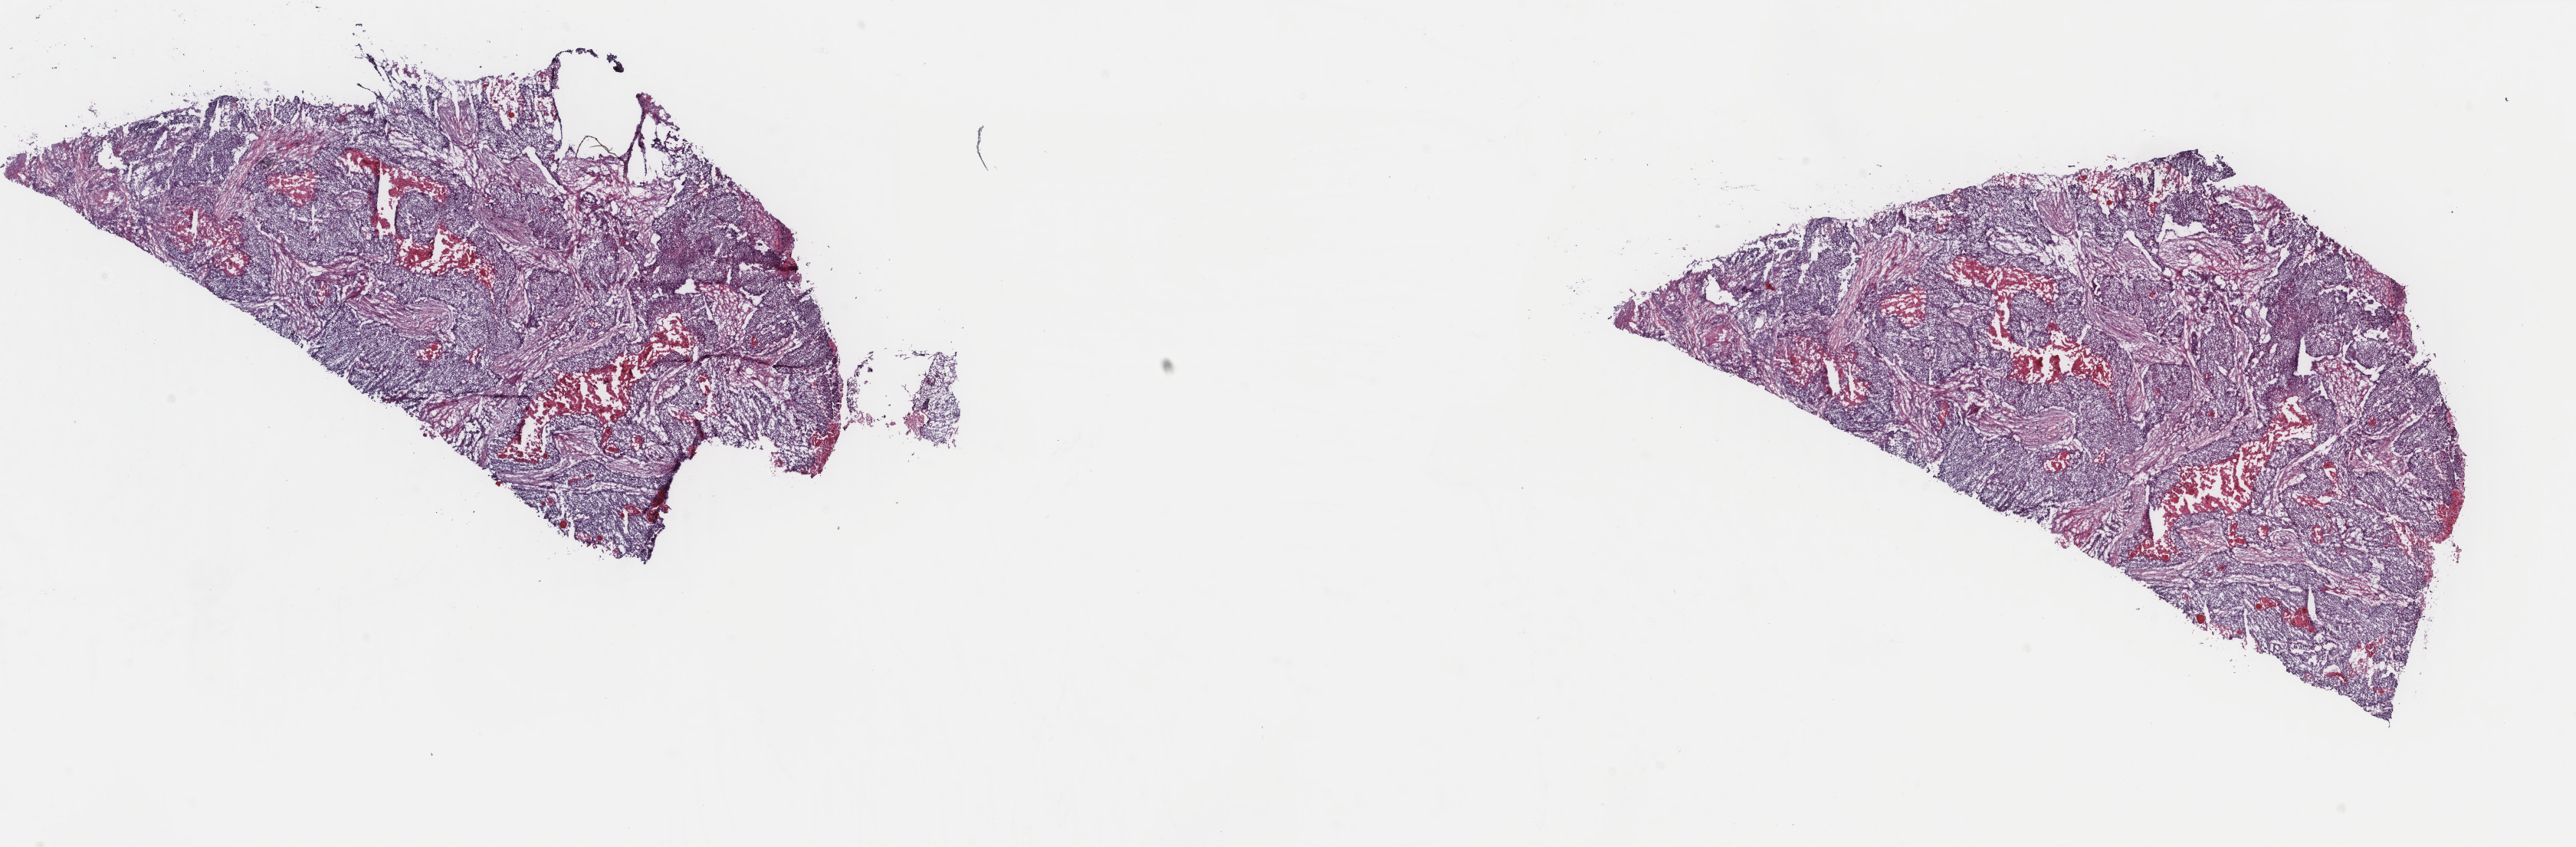
Whole-slide histology image, H&E-stained — whole scanned area (about 26.7 x 8.8 mm) shown as a low-resolution overview, frozen section, primary tumour sample from the lung. Patient: male, age at initial diagnosis 46 years.
Diagnosis: Squamous cell carcinoma, NOS (lower lobe, lung).